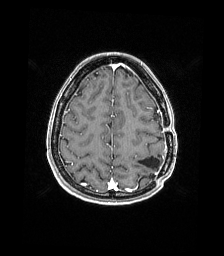
Brain MRI from a brain-tumour surgery series, one axial slice; position 50 of 176 along the scan axis; T1-weighted post-contrast; 224 × 256 image matrix, field of view 224 × 256 mm. Case-level facts recorded for this patient, not image findings: histopathology: Atypical meningioma; WHO grade: 2.
Outlined on this slice (manually delineated by an expert):
- previous resection cavity: bounding box <139,157,160,169> (left, top, right, bottom; pixels)